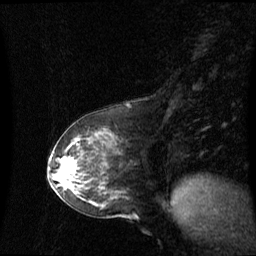
Breast MRI (dynamic contrast-enhanced), one sagittal slice; position 29 of 60 along the scan axis; dynamic contrast-enhanced series, image 2 of 3 at this slice position (ordered by acquisition); 1.5 T; TE 4.2 ms, TR 8.4 ms; 2.1 mm slice thickness; 256 × 256 image matrix. Patient: female, 59 years. Case-level facts recorded for this patient, not image findings: setting: breast cancer imaged before/during neoadjuvant chemotherapy; receptor status: HR-positive, HER2-negative.
Outlined on this slice (semi-automatically segmented with operator editing):
- analysis volume of interest (the breast-tissue region the enhancement analysis was run in; not a lesion): box from (x=55, y=148) to (x=89, y=191) px
- tumour enhancement mask (voxels above the 70 % enhancement threshold inside the analysis volume of interest): (x=63, y=161)–(x=76, y=172)